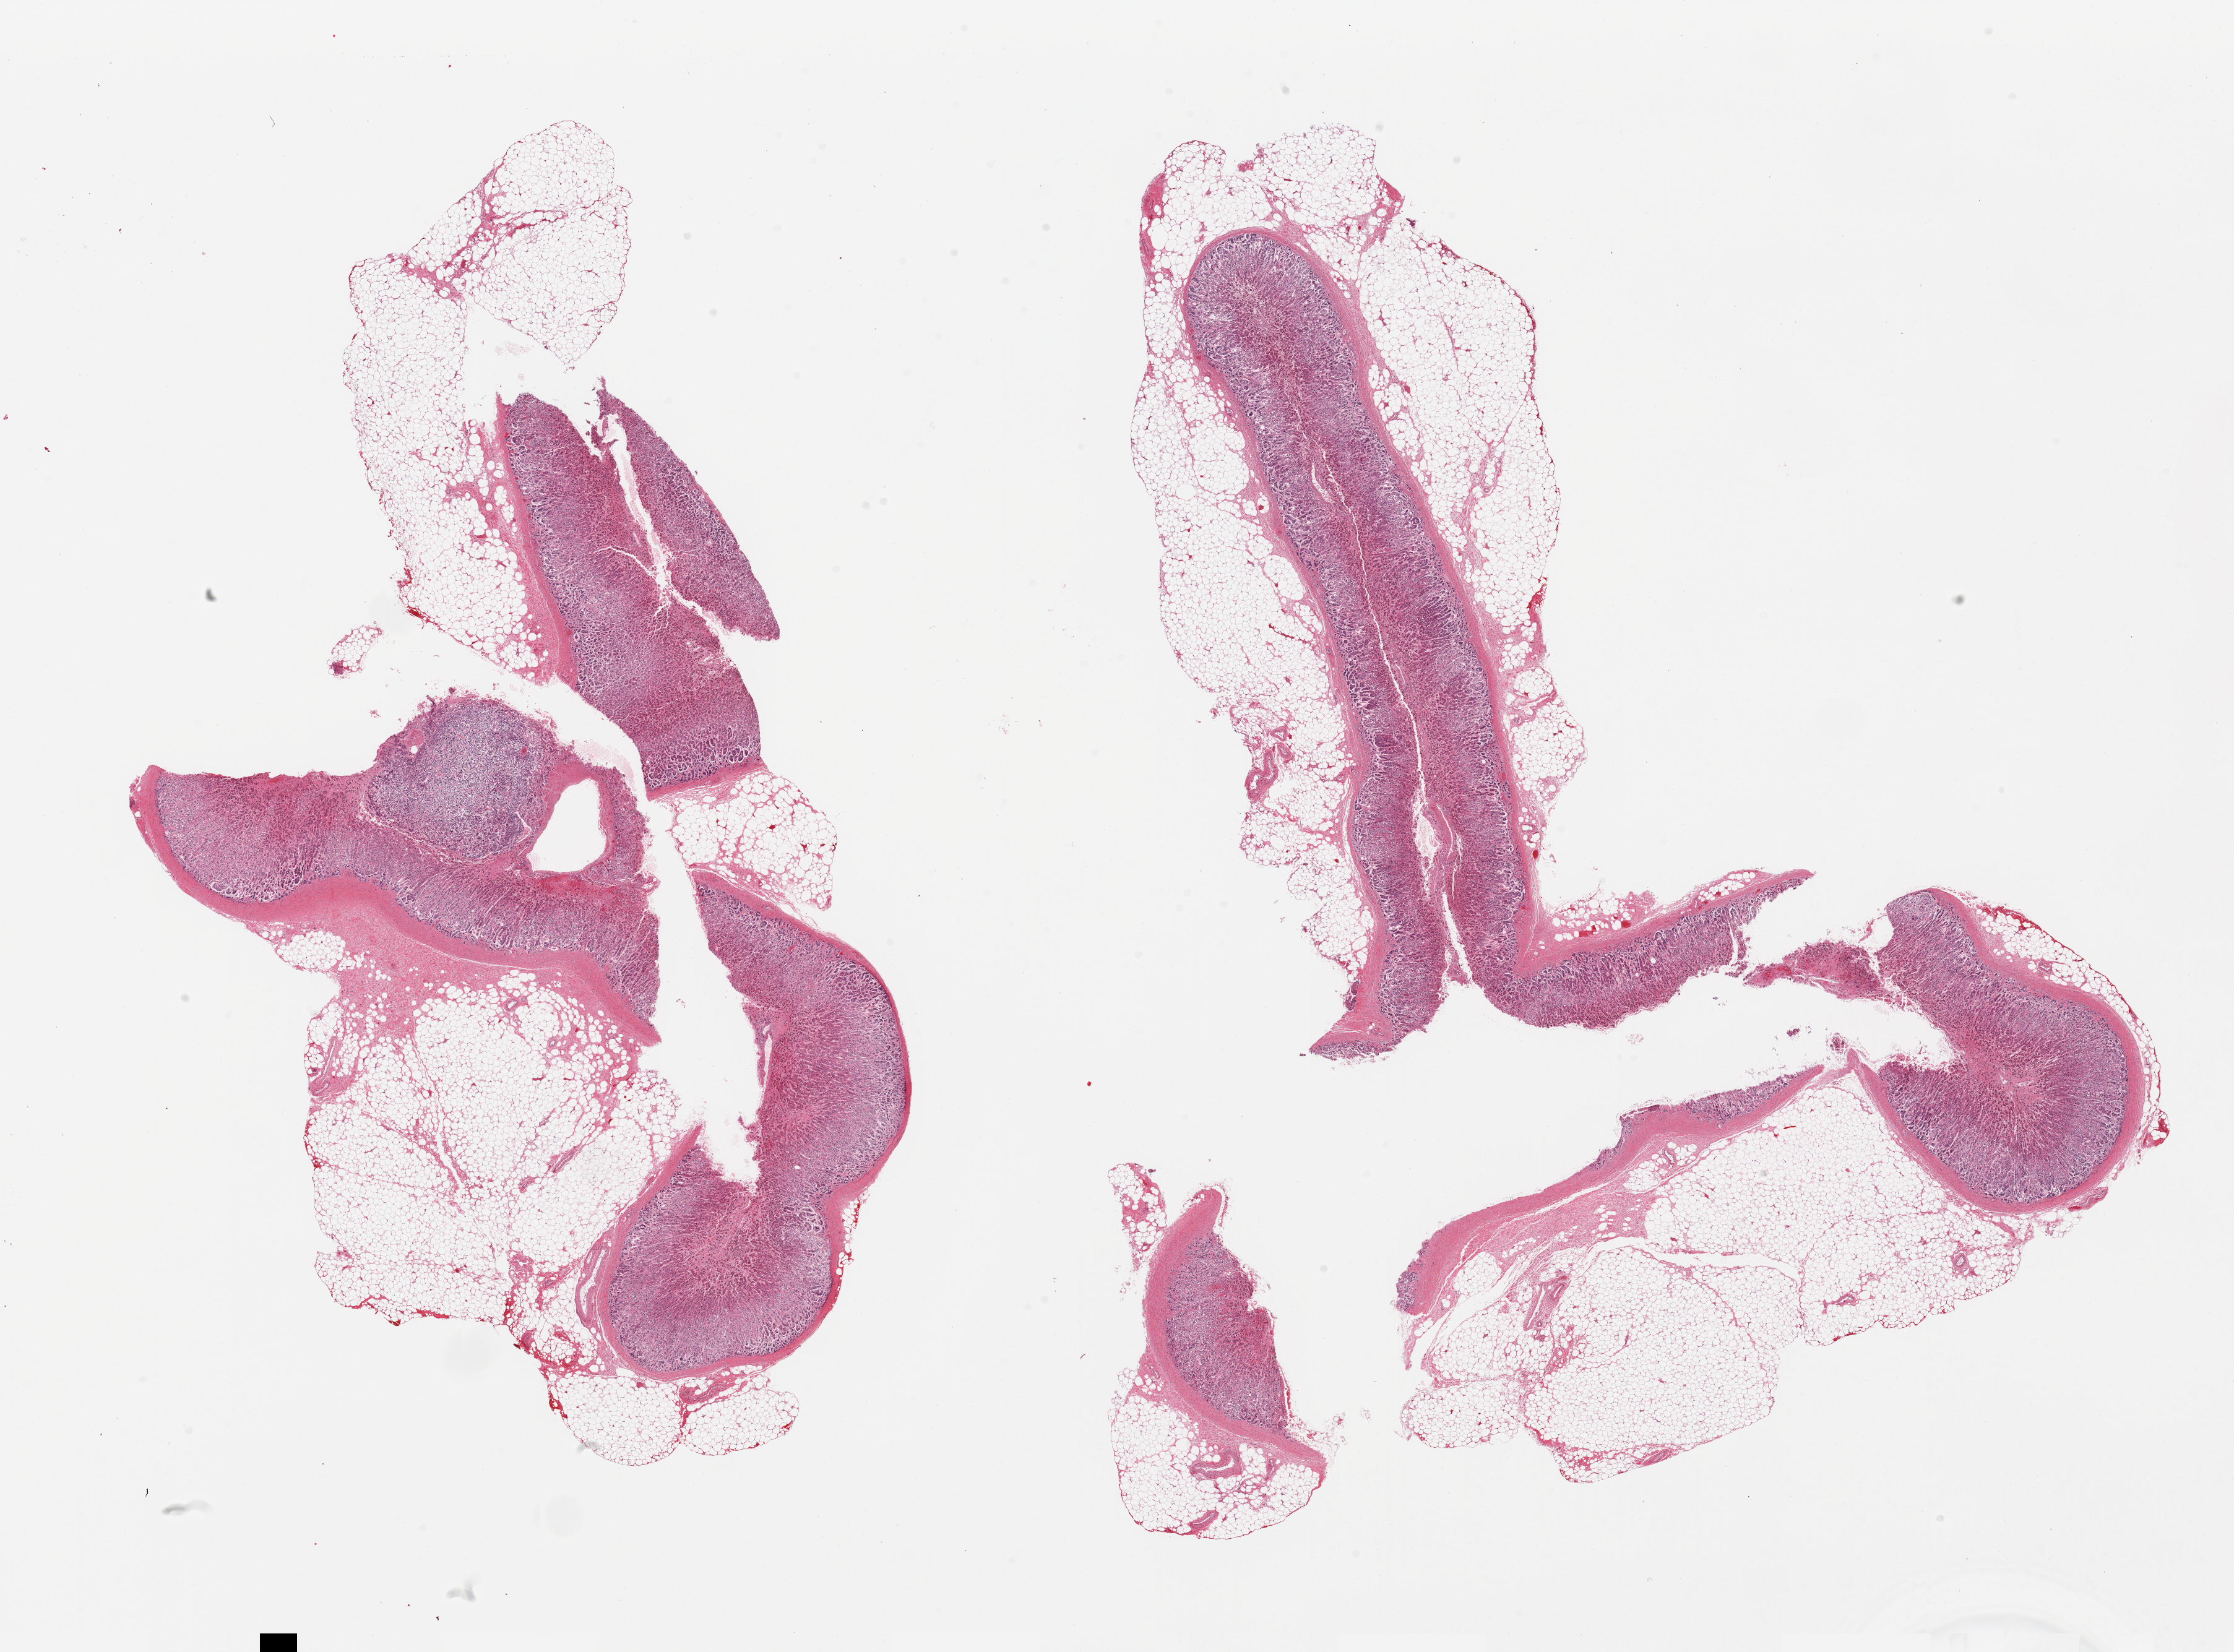
Whole-slide image, H&E stain, brightfield, whole scanned area (about 28.5 x 21.1 mm) shown as a low-resolution overview, PAXgene-fixed paraffin-embedded (PFPE) section, sampled site (target tissue): adrenal gland, tissue donor sample.
Pathologist's review note for this sample: 2 pieces; 50% external fat.